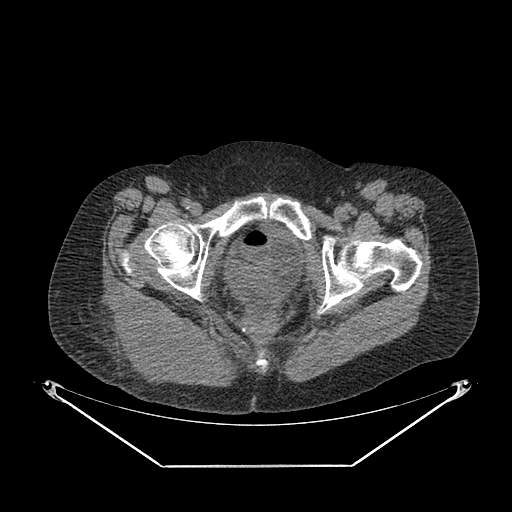
CT of an extremity soft-tissue mass (from a PET/CT study), one axial slice. Position 51 of 267 along the scan axis. Reconstruction kernel SOFT. Soft-tissue window (W 400 / L 40 HU). 3.75 mm slice thickness. 512 × 512 image matrix. Female patient. From the clinical record (not read from this slice): histological type: spindle cell suggestive of myxofibrosarcoma; grade: intermediate; site of the primary tumour: right buttock.
Structures marked on this image (expert contour drawn on MRI and transferred to this co-registered scan by the dataset authors):
- gross tumour volume (mass): bounding box <105,297,204,385> (left, top, right, bottom; pixels)